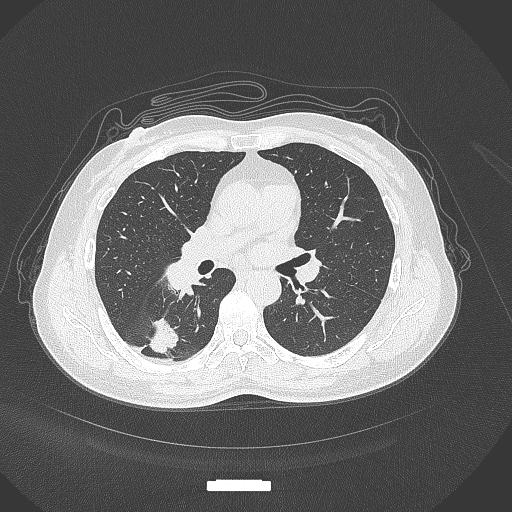
Chest CT, one axial slice; slice 168 of 352 in the series (ordered by position); 120 kVp; lung window (W 1500 / L -600 HU); 1 mm slice thickness; 512 × 512 image matrix. Patient: female, 55 years. Case-level facts recorded for this patient, not image findings: clinical TNM (as recorded): T1c N1 M0.
Annotated regions visible in this slice (bounding box drawn by a radiologist):
- lung tumour (recorded histology: adenocarcinoma): box from (x=148, y=314) to (x=182, y=355) px